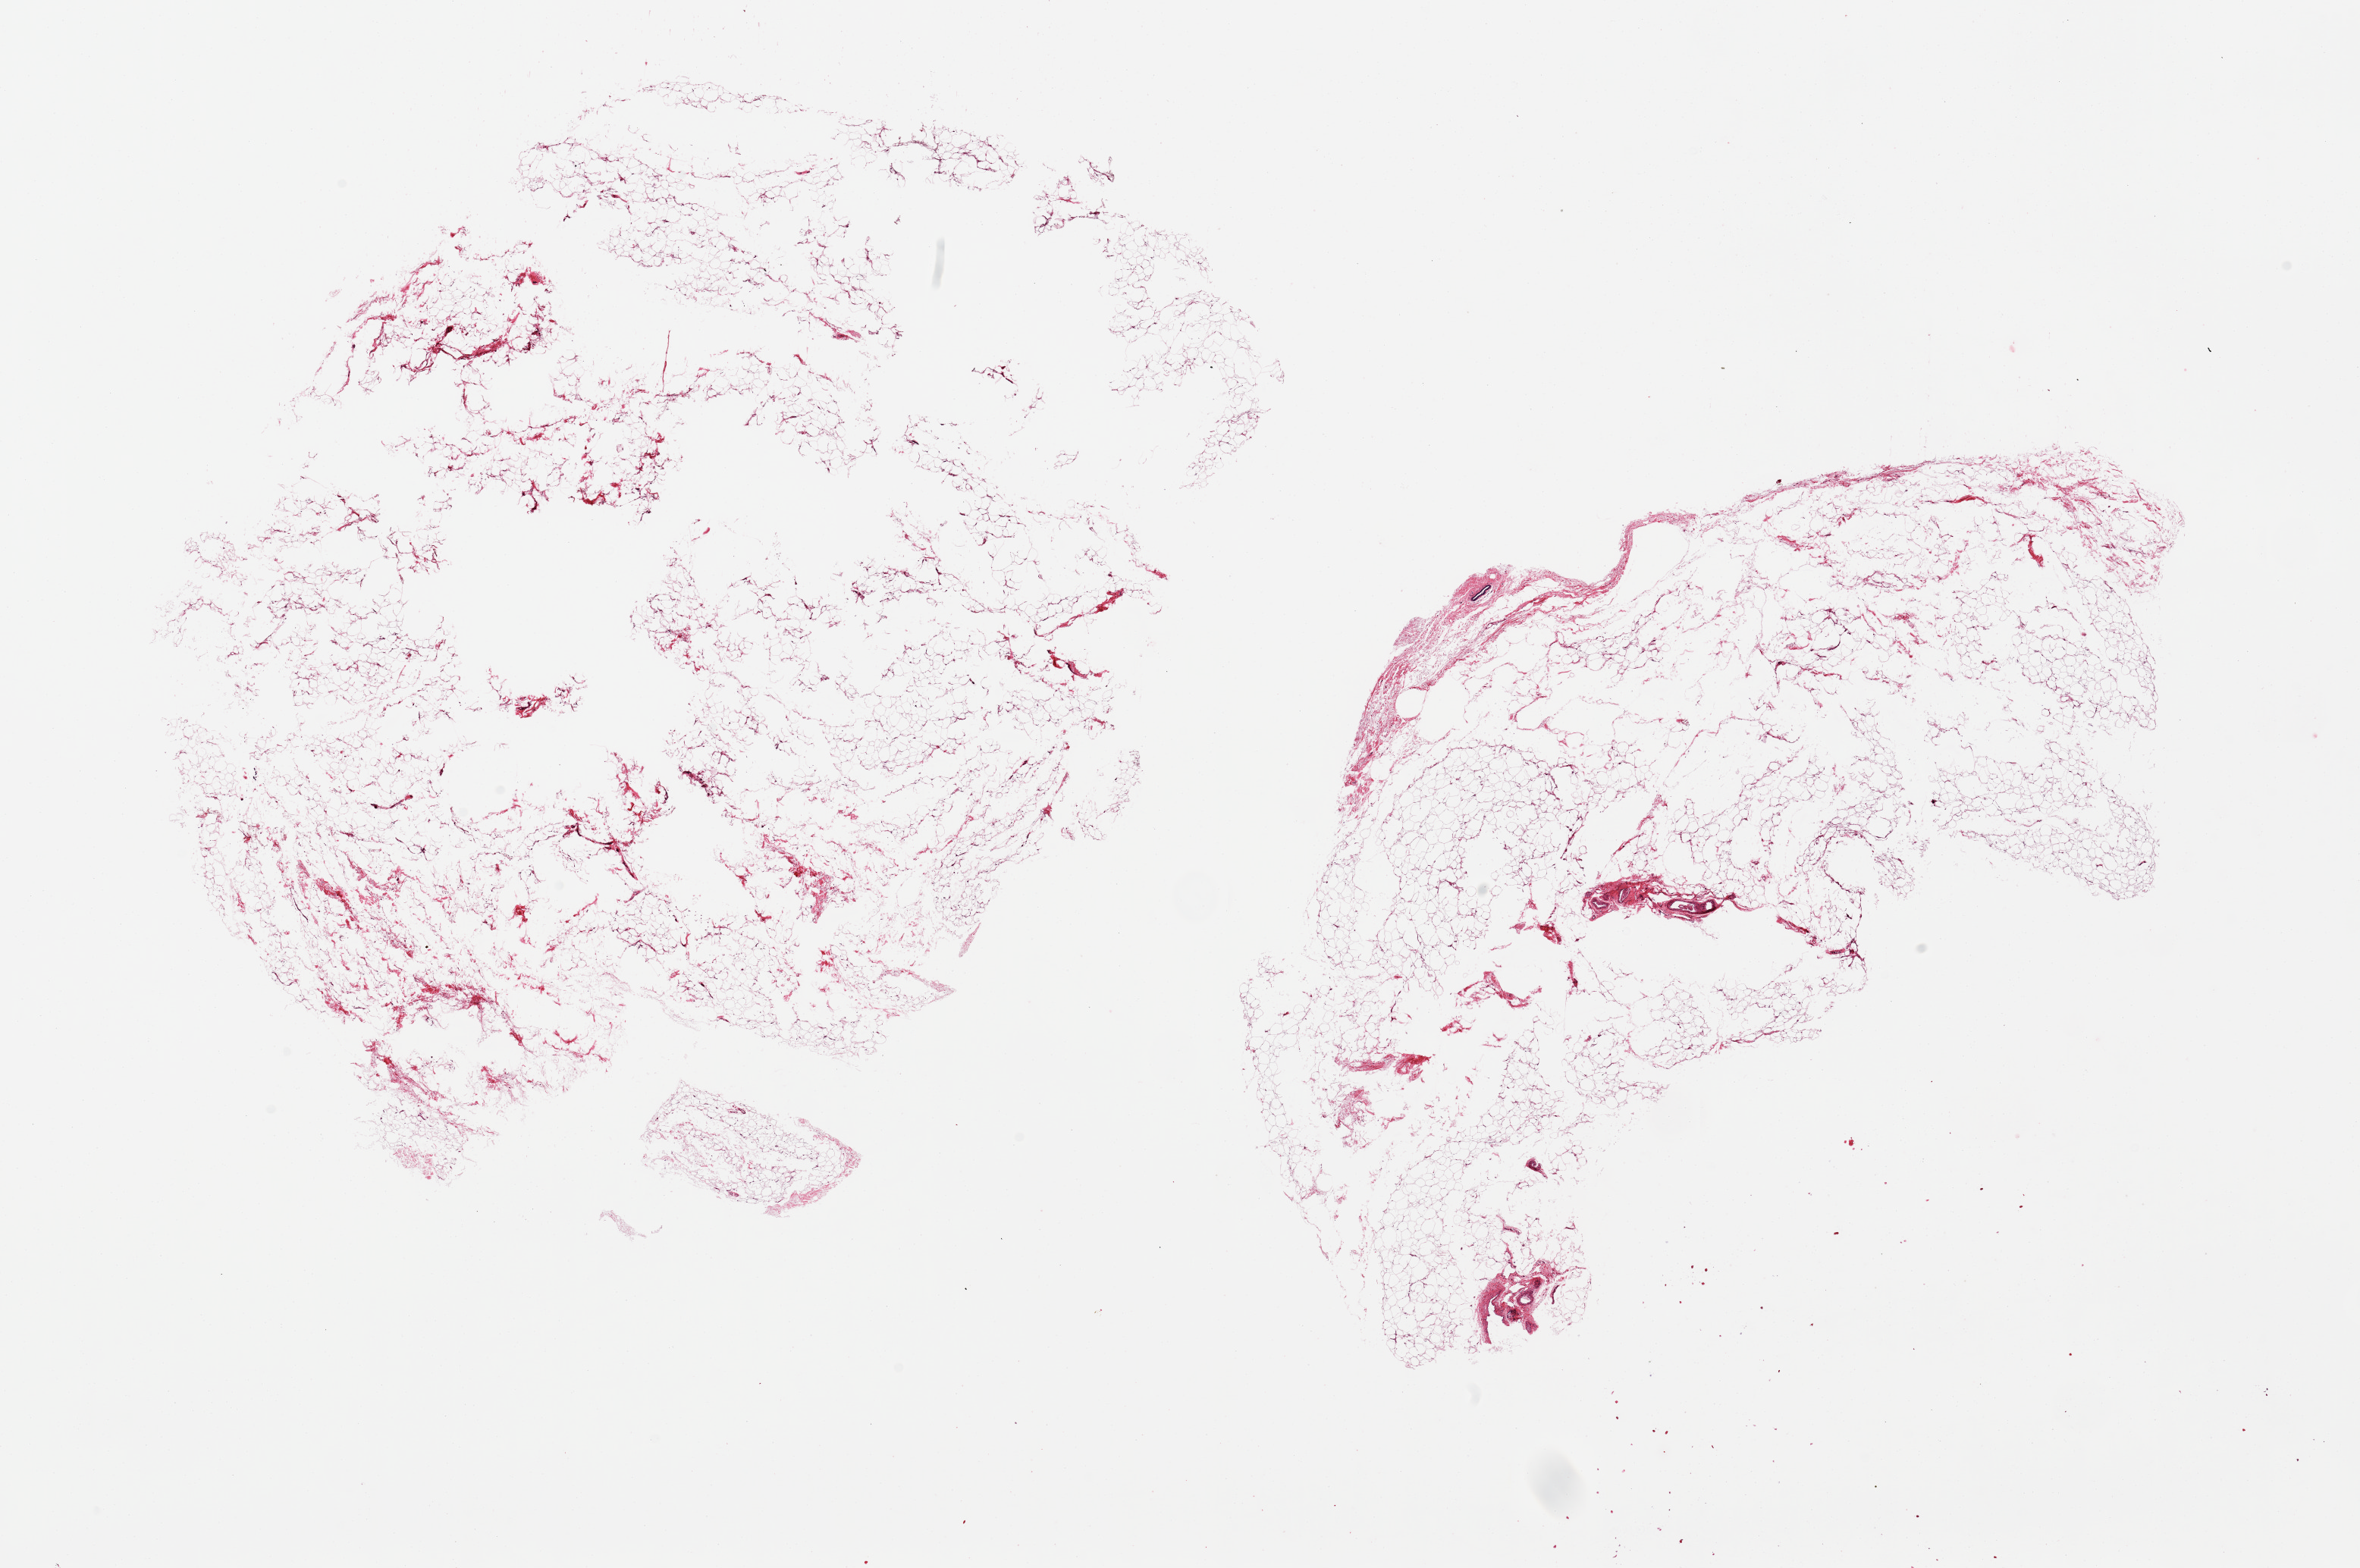
H&E whole-slide image, whole scanned area (about 24.6 x 16.4 mm) shown as a low-resolution overview; PAXgene-fixed, paraffin-embedded tissue; sampled site (target tissue): breast; donor tissue sample. Donor: female.
* reviewer comment on this tissue sample: 2 pieces; only one duct seen